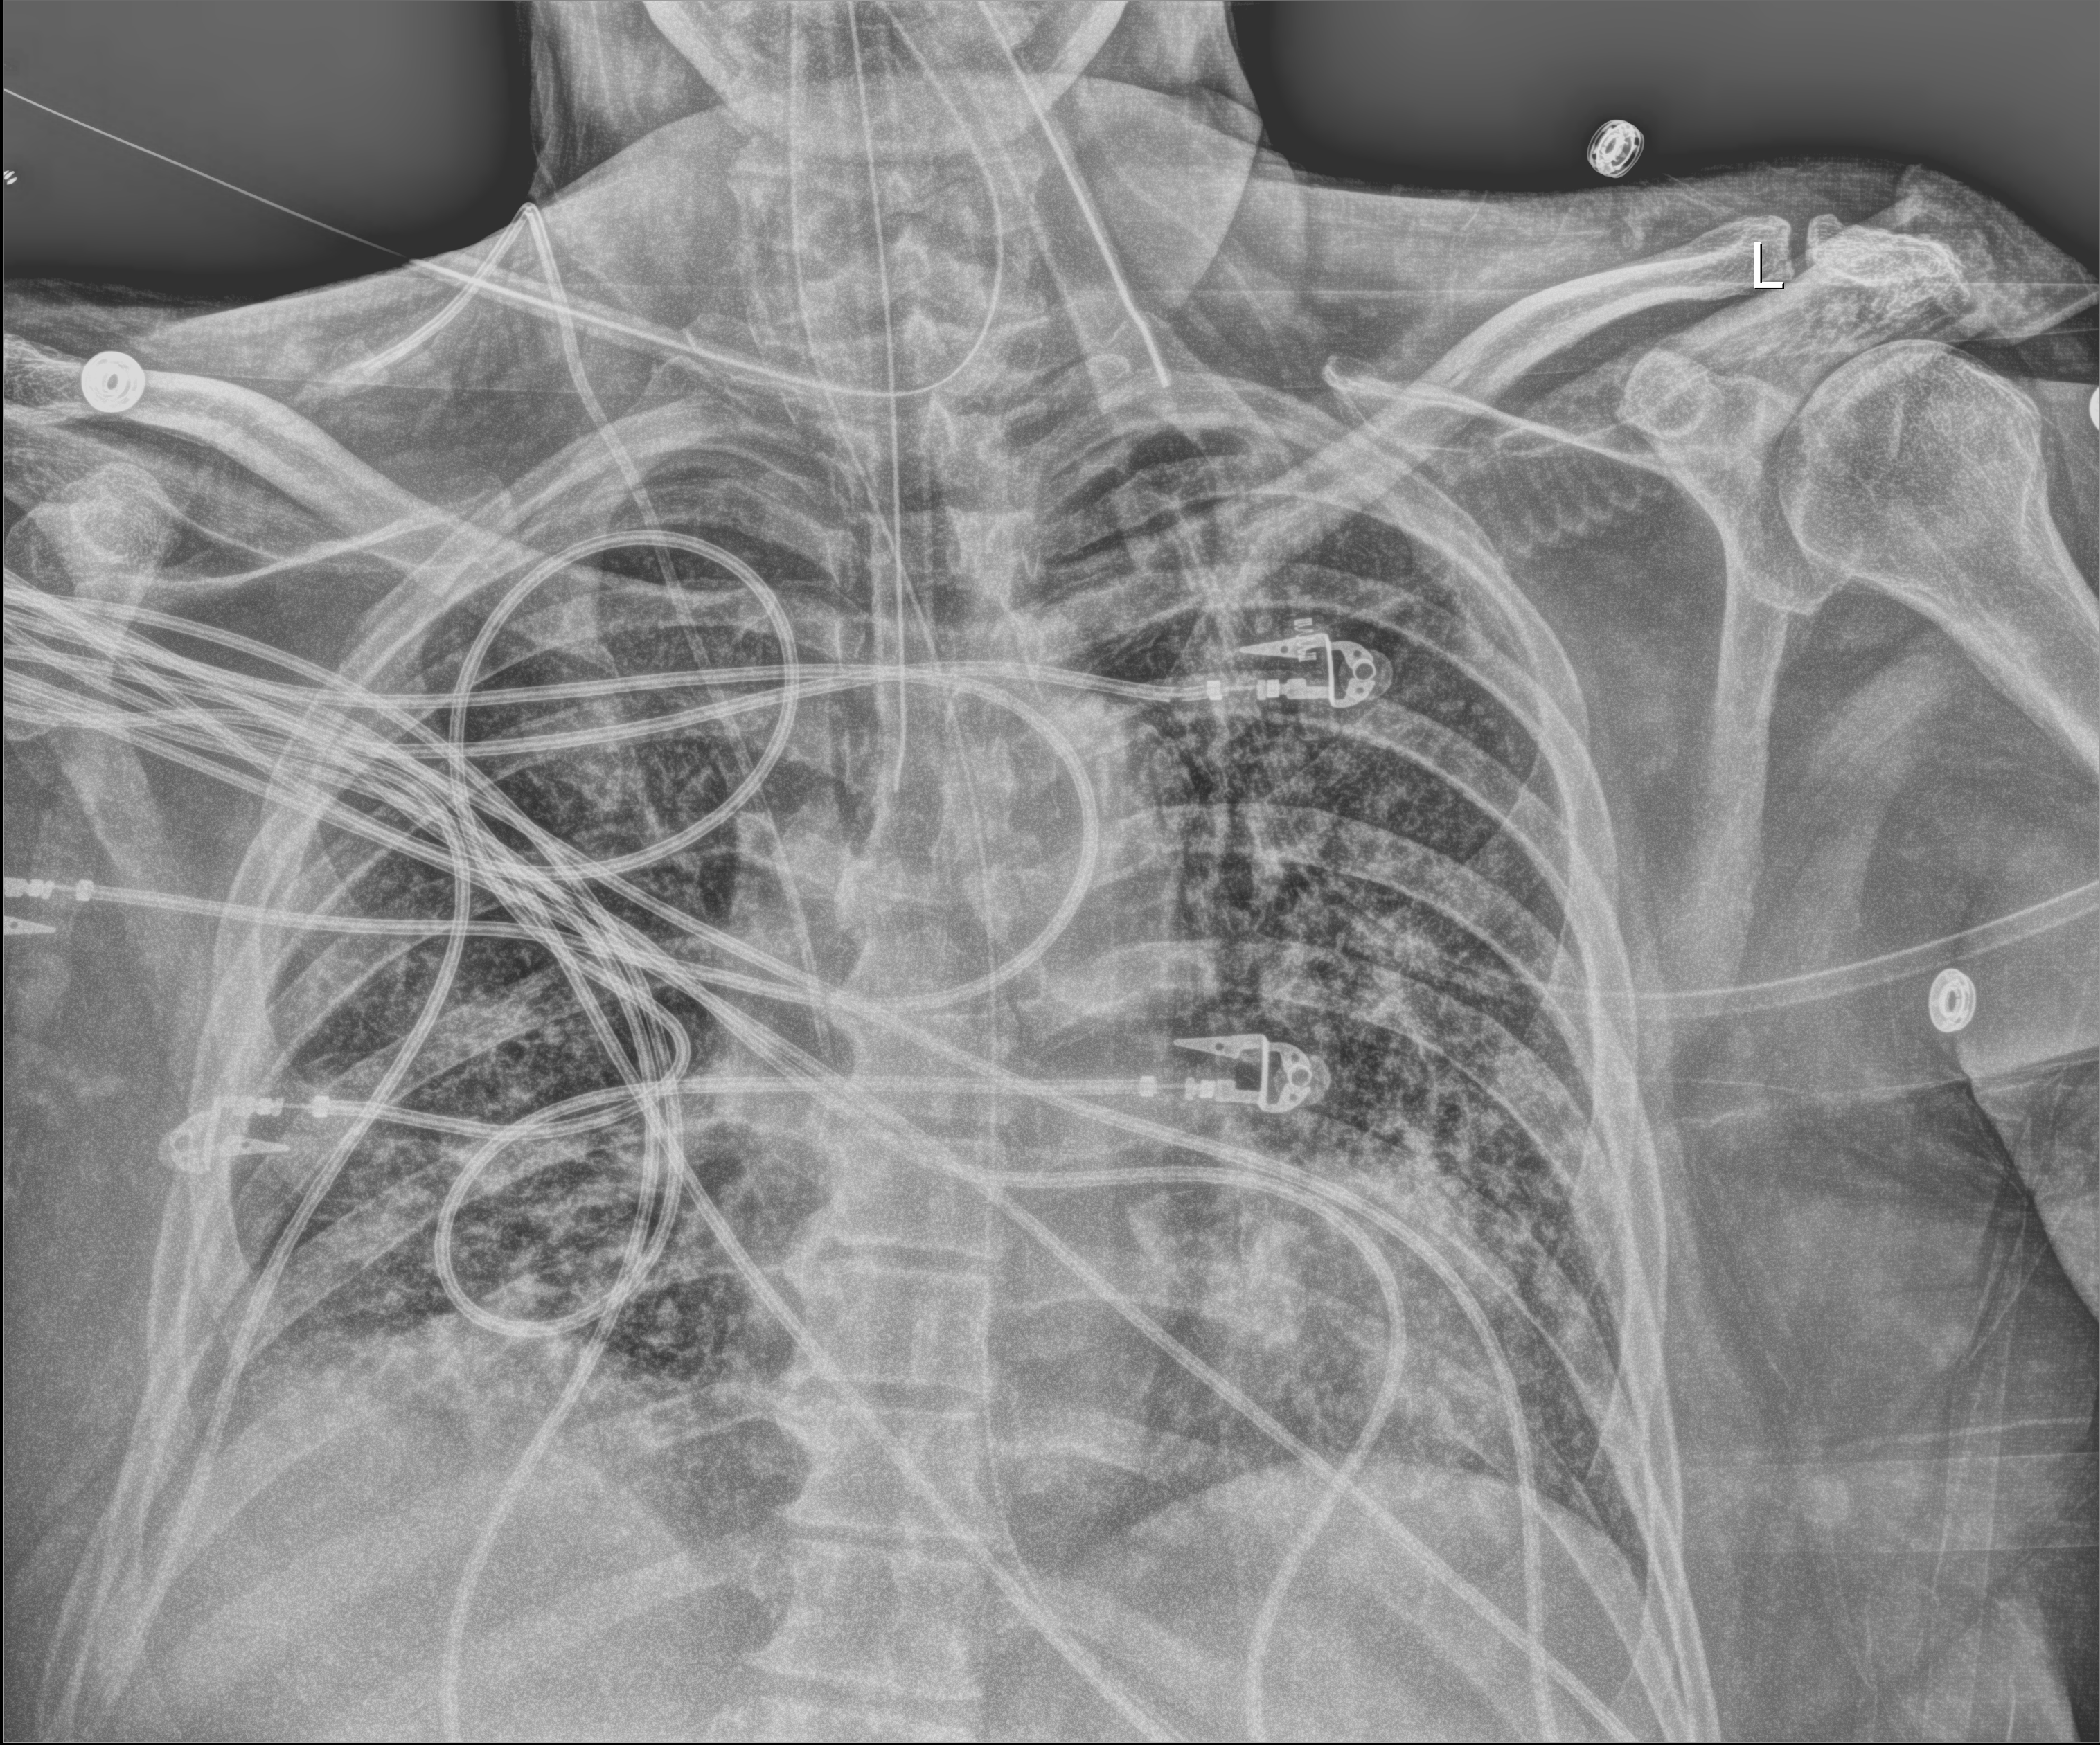
Portable chest radiograph; anteroposterior (AP) projection. Male patient hospitalised with COVID-19, age 60–74 years.
Hospital-stay facts (about this admission, not read from this image; timing relative to this image not recorded):
- admitted to intensive care during this hospital stay: yes
- diabetes (admission record): no